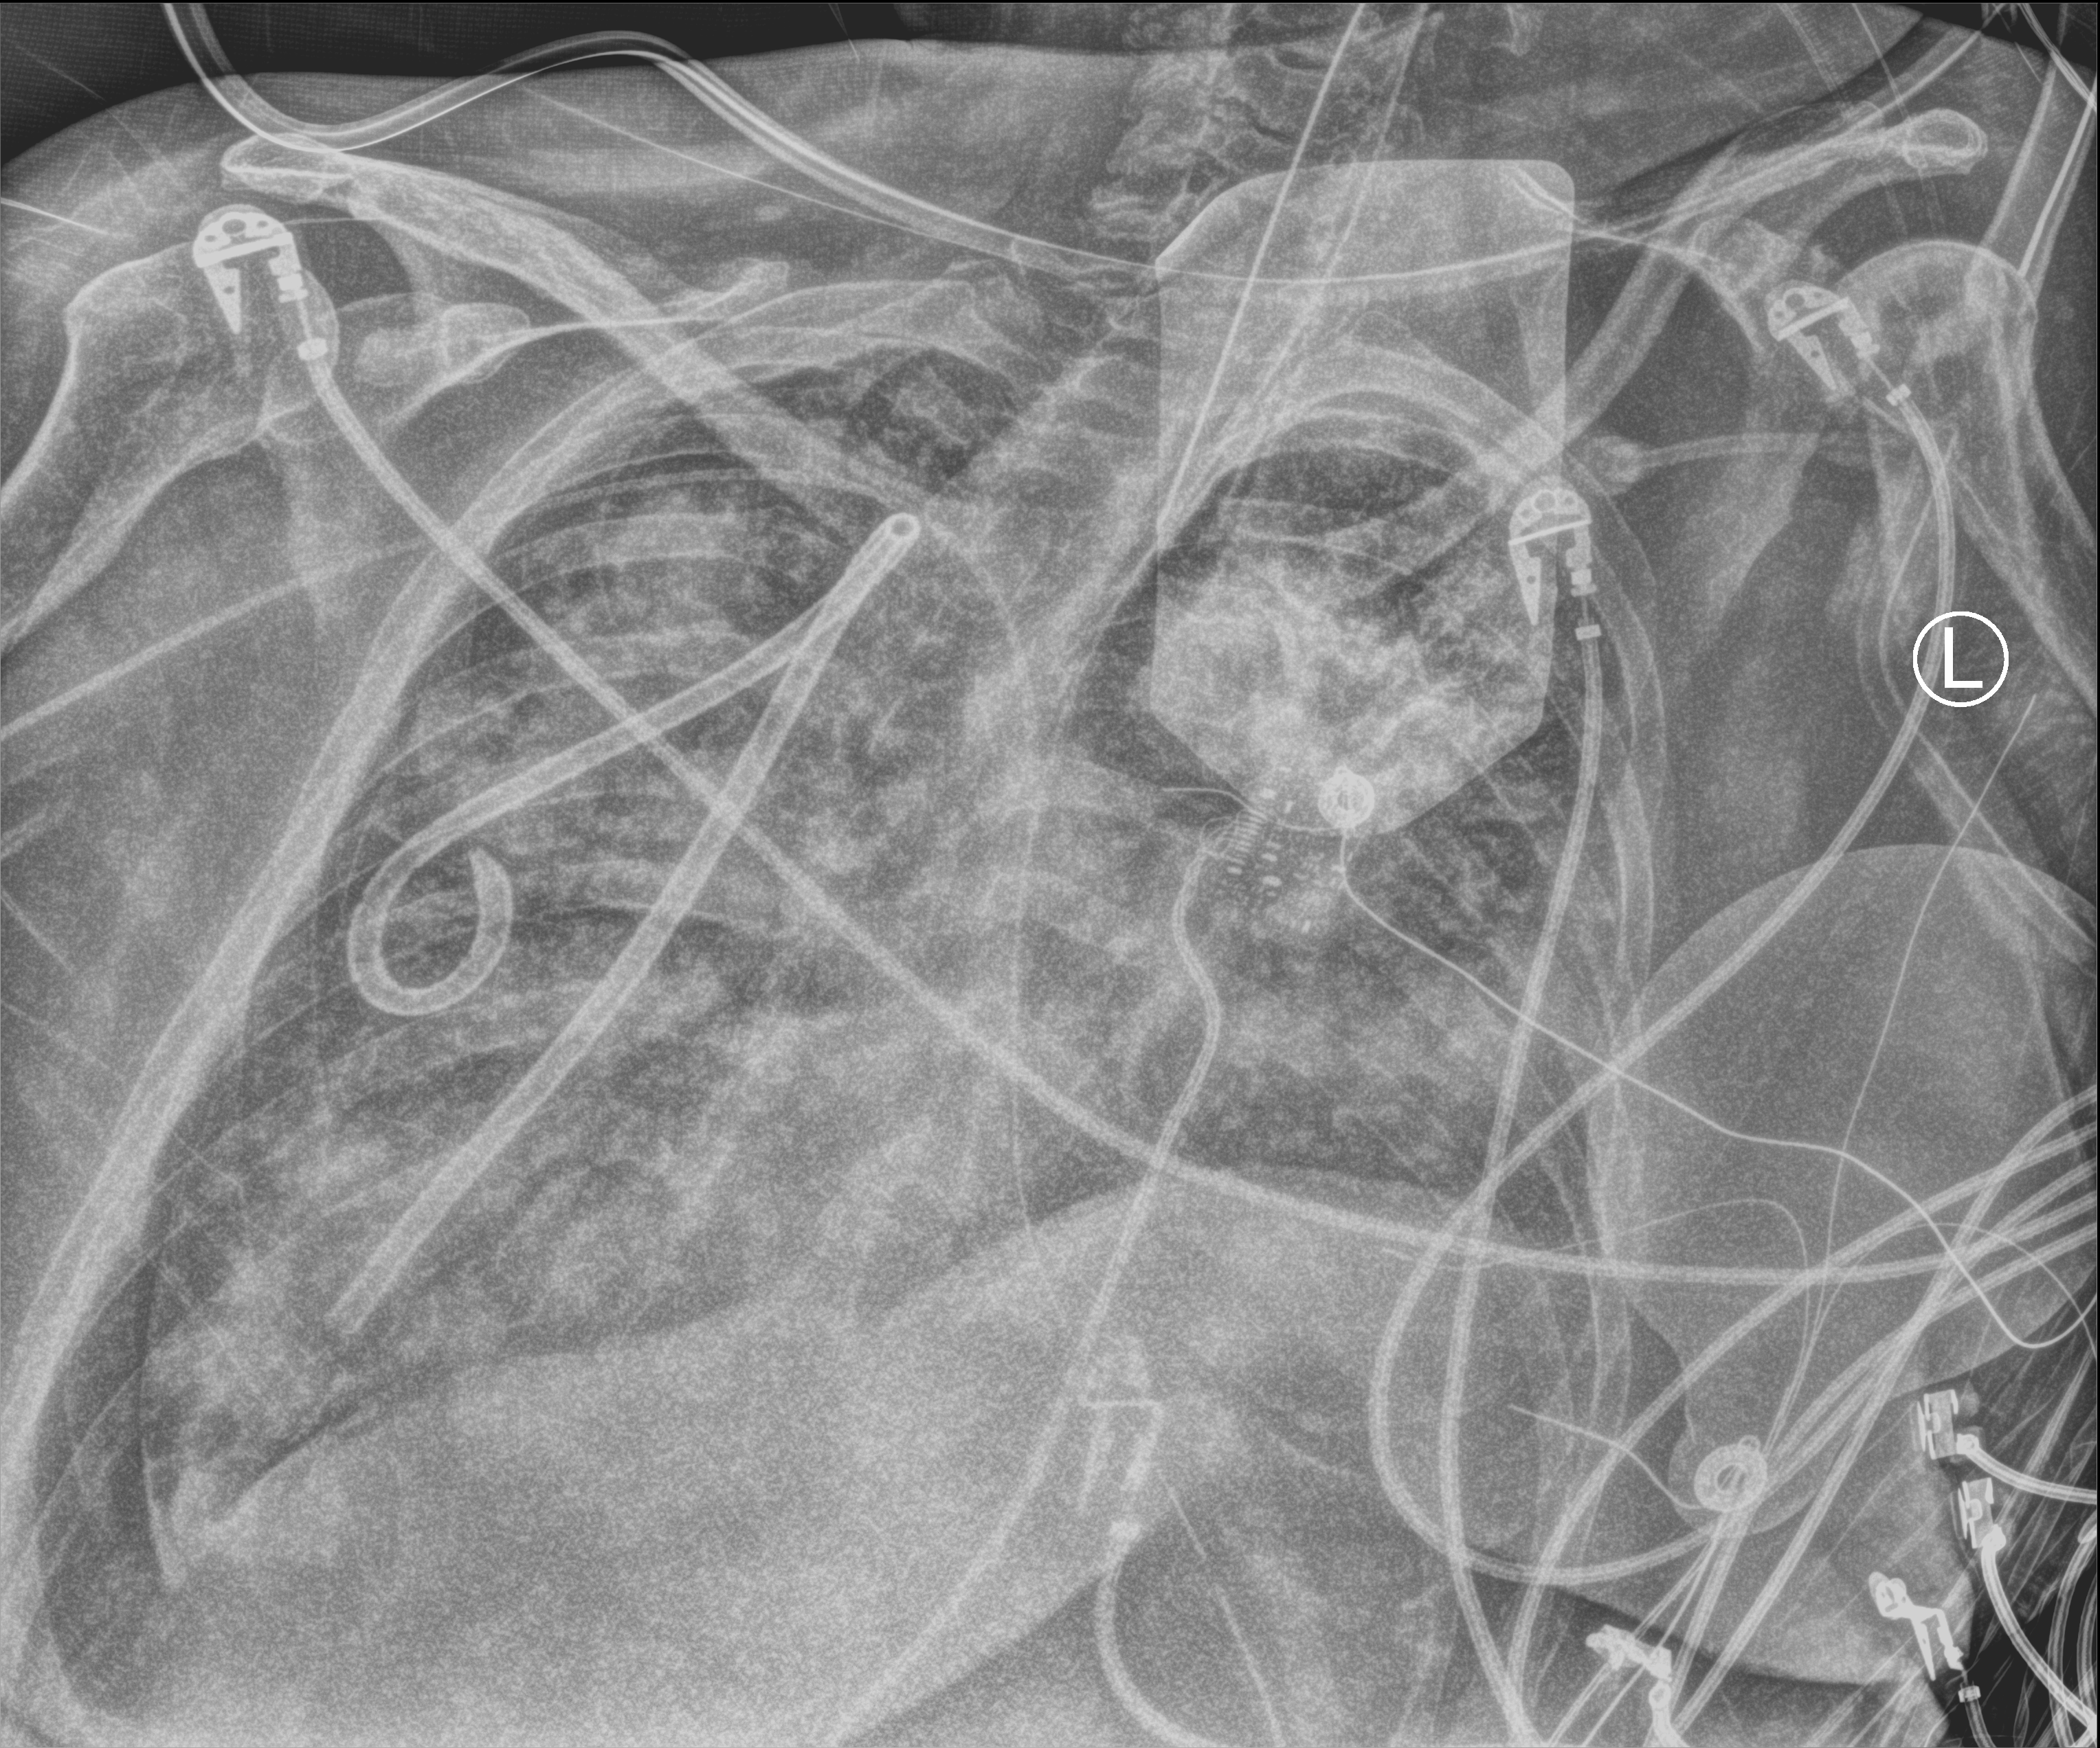
Portable chest radiograph. Patient hospitalised with COVID-19, aged 18–59 years.
Admission-level facts for this patient (not findings on this image; timing relative to this image not recorded):
- mechanically ventilated during this hospital stay: yes